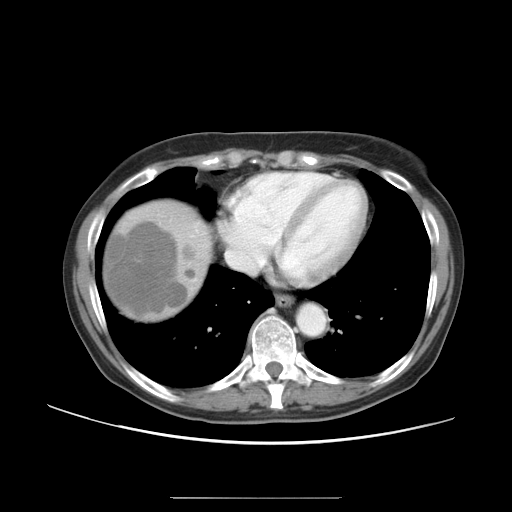
Contrast-enhanced abdominal CT, one axial slice. Position 44 of 50 along the scan axis. Reconstruction kernel STANDARD. 120 kVp. Intravenous contrast given. Soft-tissue window (W 400 / L 40 HU). 5 mm slice thickness. 512 × 512 image matrix. Female patient, age 58 years. From the clinical record (not read from this slice): diagnosis: colorectal cancer liver metastases, imaged before liver resection.
Annotated regions visible in this slice (manually delineated by an expert):
- hepatic veins: box from (x=226, y=239) to (x=267, y=272) px
- liver: (x=104, y=205)–(x=207, y=318)
- liver metastasis: (x=106, y=220)–(x=187, y=315)